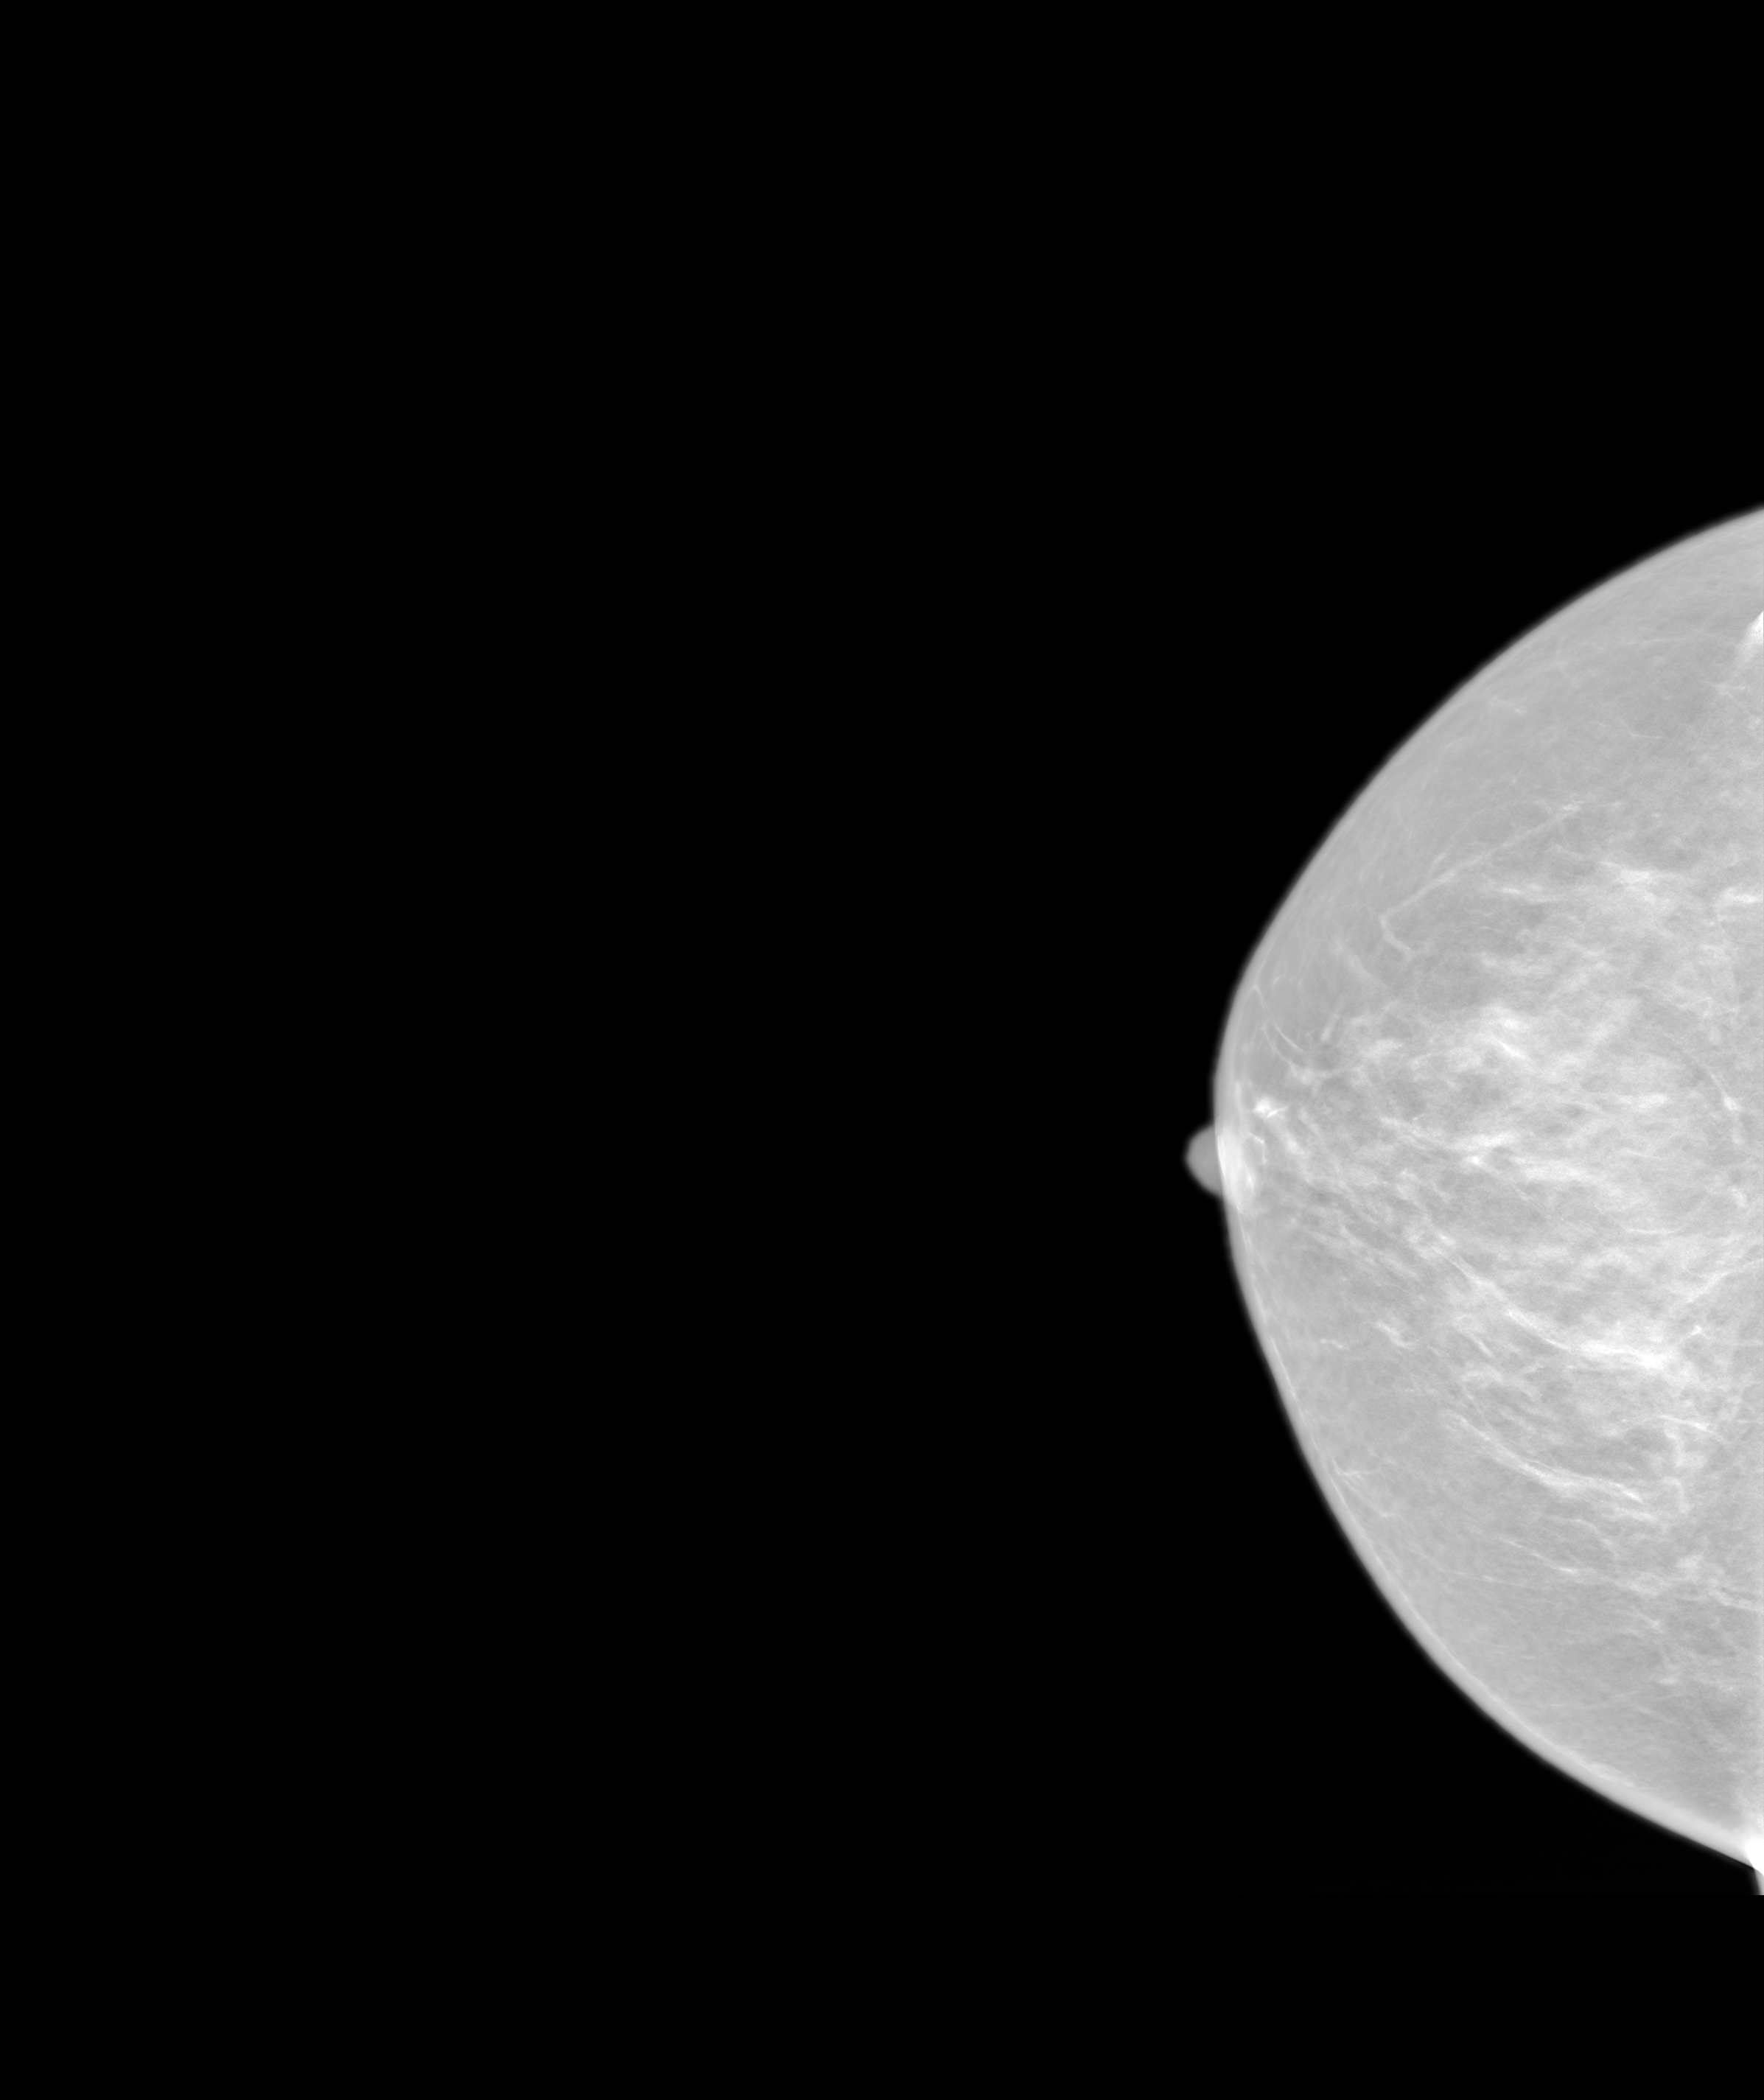
Synthesized 2-D mammogram reconstructed from digital breast tomosynthesis, right breast, cranio-caudal projection, annual screening mammography examination. Patient: female, 48 years.
BI-RADS breast density category at the screening exam (both breasts, scale 1–4): 3. Final BI-RADS assessment for this screening round (tomosynthesis exam, both breasts): category 1. Recall: no recall after this screen.